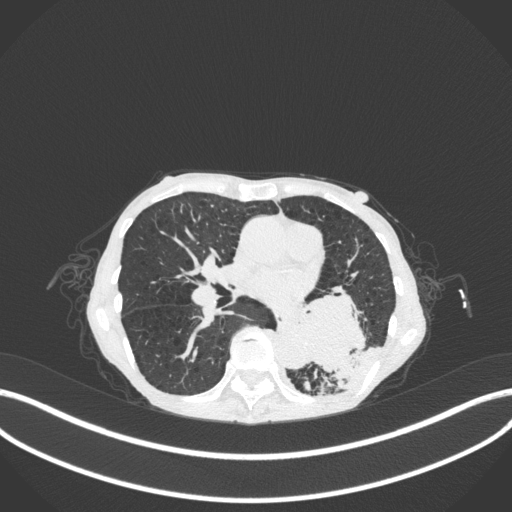
Chest CT, one axial slice; position 135 of 347 along the scan axis; reconstruction kernel B31f; 120 kVp; lung window (W 1500 / L -600 HU); 1 mm slice thickness; 512 × 512 image matrix, field of view 400 × 400 mm. Female patient, age 70 years. From the clinical record (not read from this slice): clinical TNM (as recorded): T3 N0 M0.
Outlined on this slice (rectangle marked by the reading radiologist):
- lung tumour (recorded histology: small cell carcinoma): bounding box <291,282,372,374> (left, top, right, bottom; pixels)